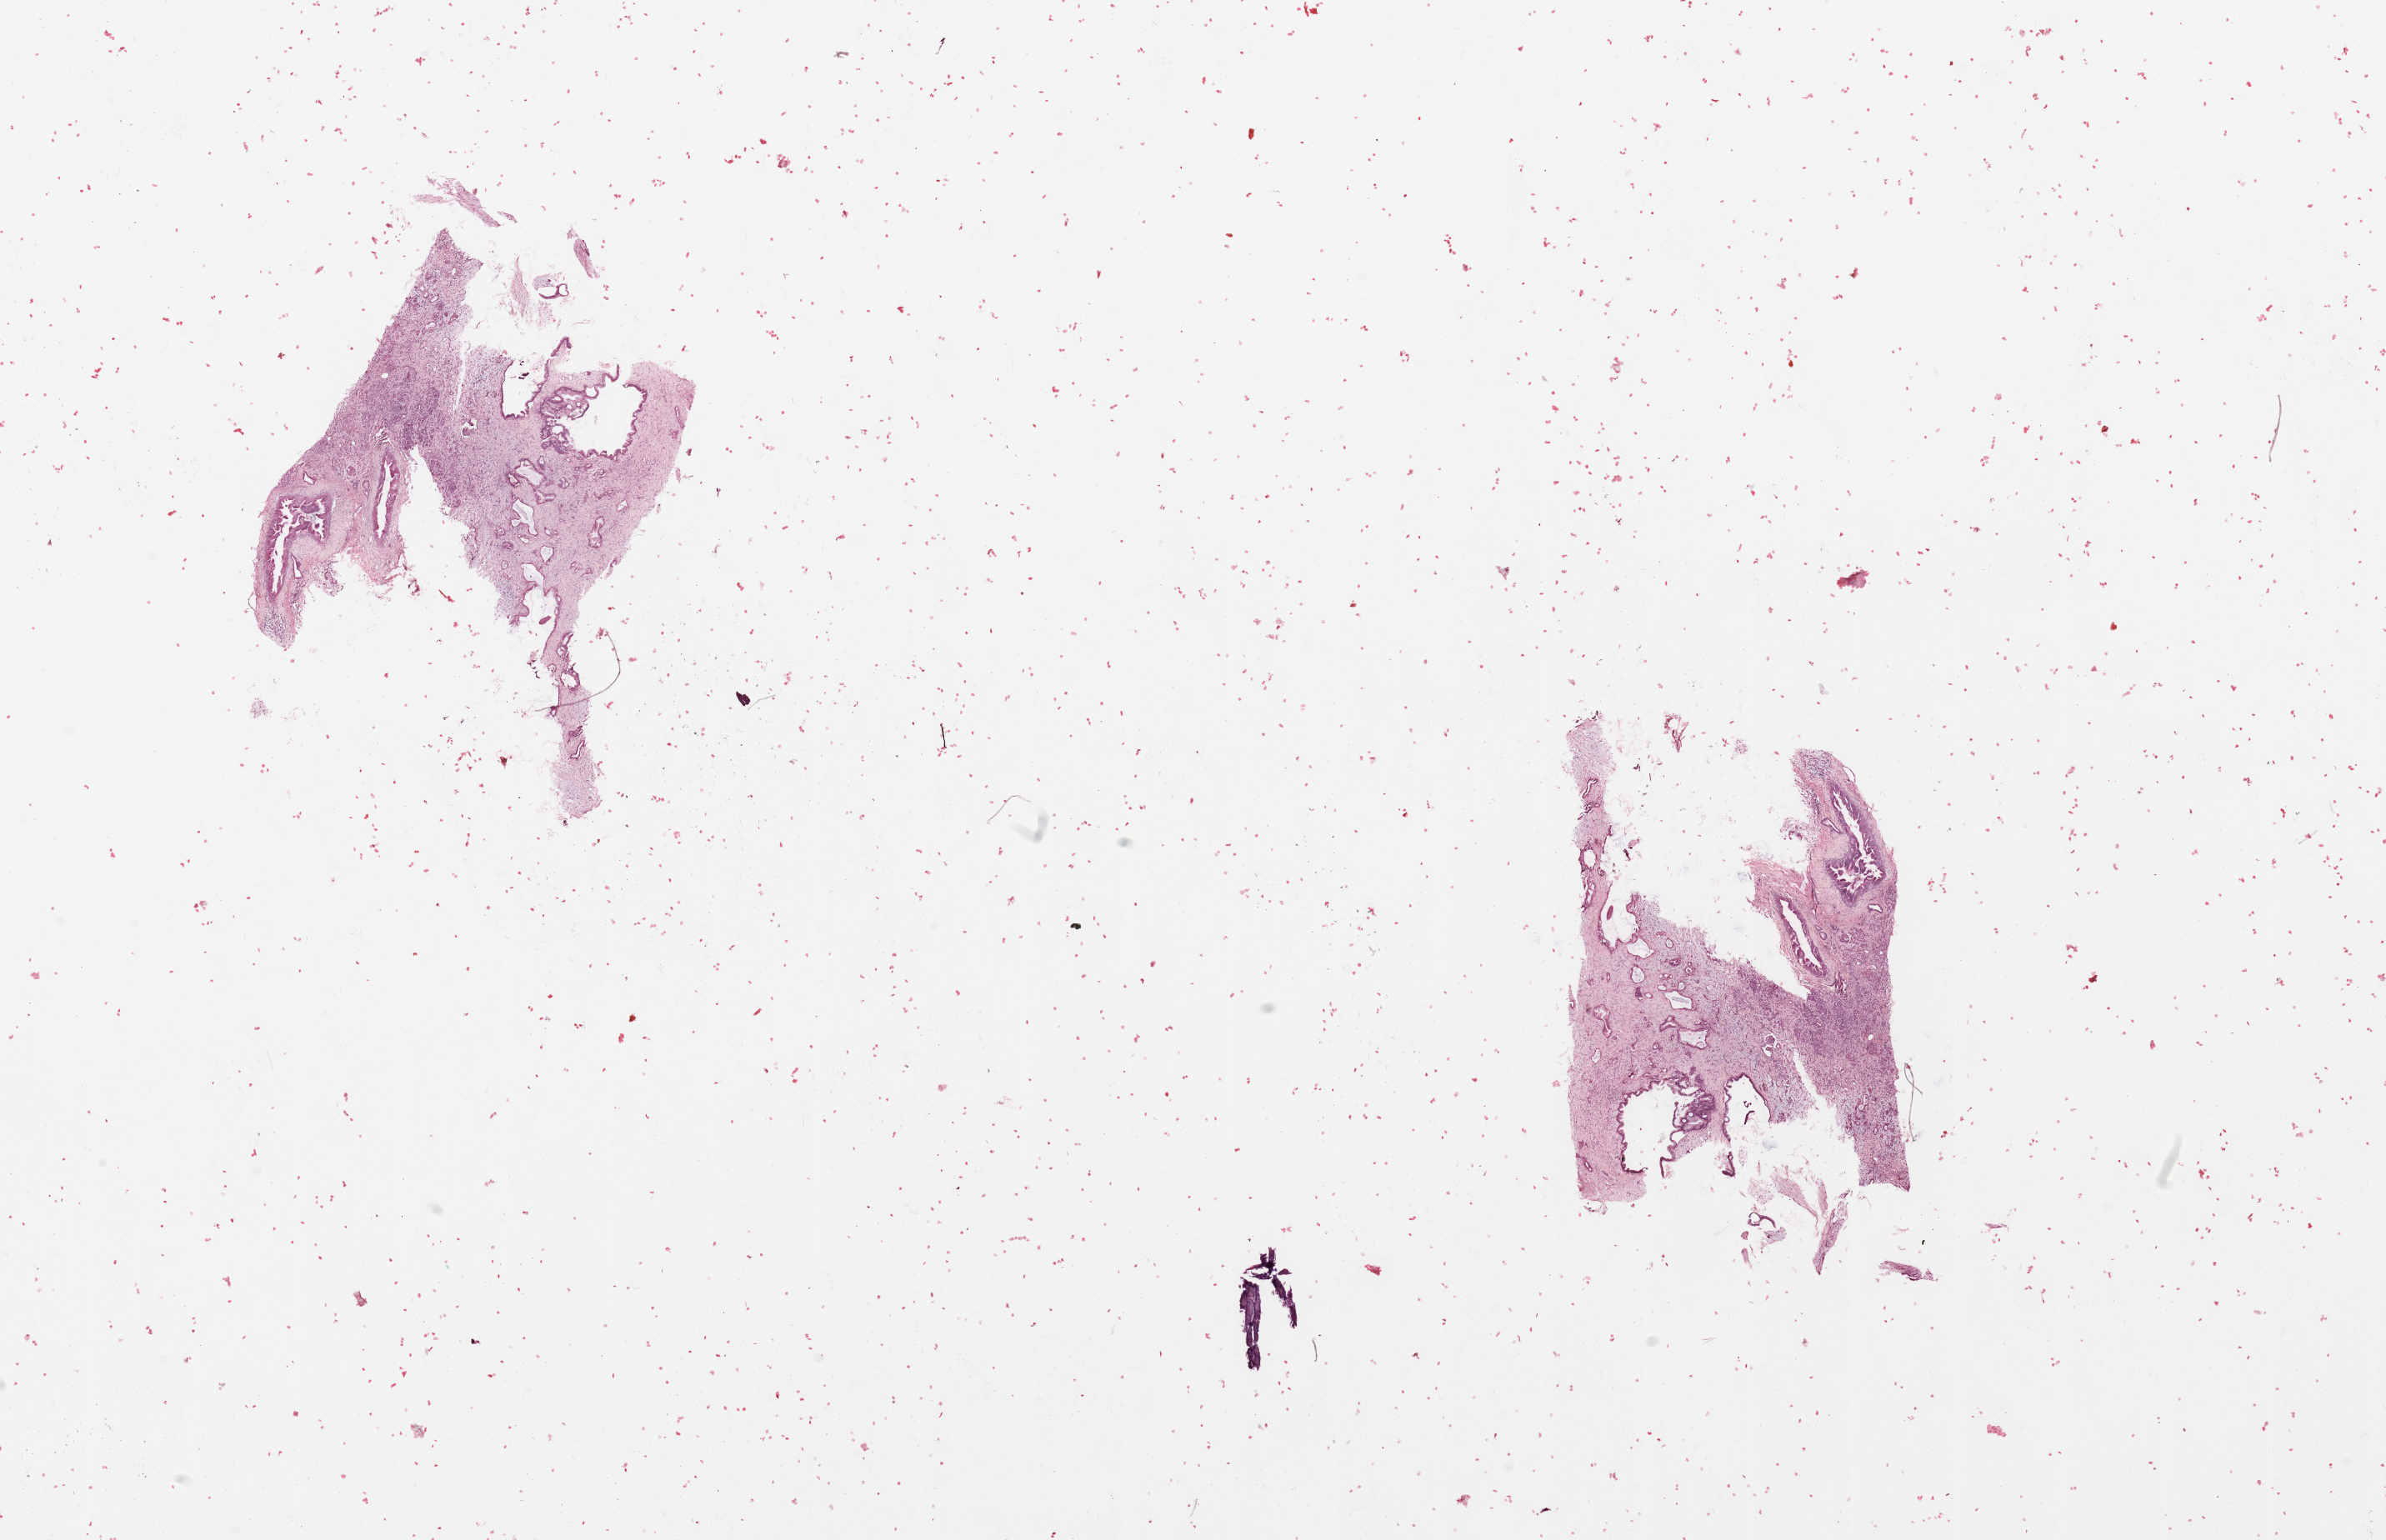
Whole-slide histology image, H&E — a low-resolution overview of the entire scanned area, about 22.6 x 14.6 mm (acquisition: 20x scan), tumour tissue sample, sampled site: pancreas. Patient: female, age 56 years. Histologic grade: G1 (well differentiated). Composition of this section per pathologist review: tumour nuclei 20%, necrosis 2%.
Primary tumour site (as recorded): head. Histologic diagnosis: Infiltrating duct carcinoma, NOS. AJCC pathologic stage: III.